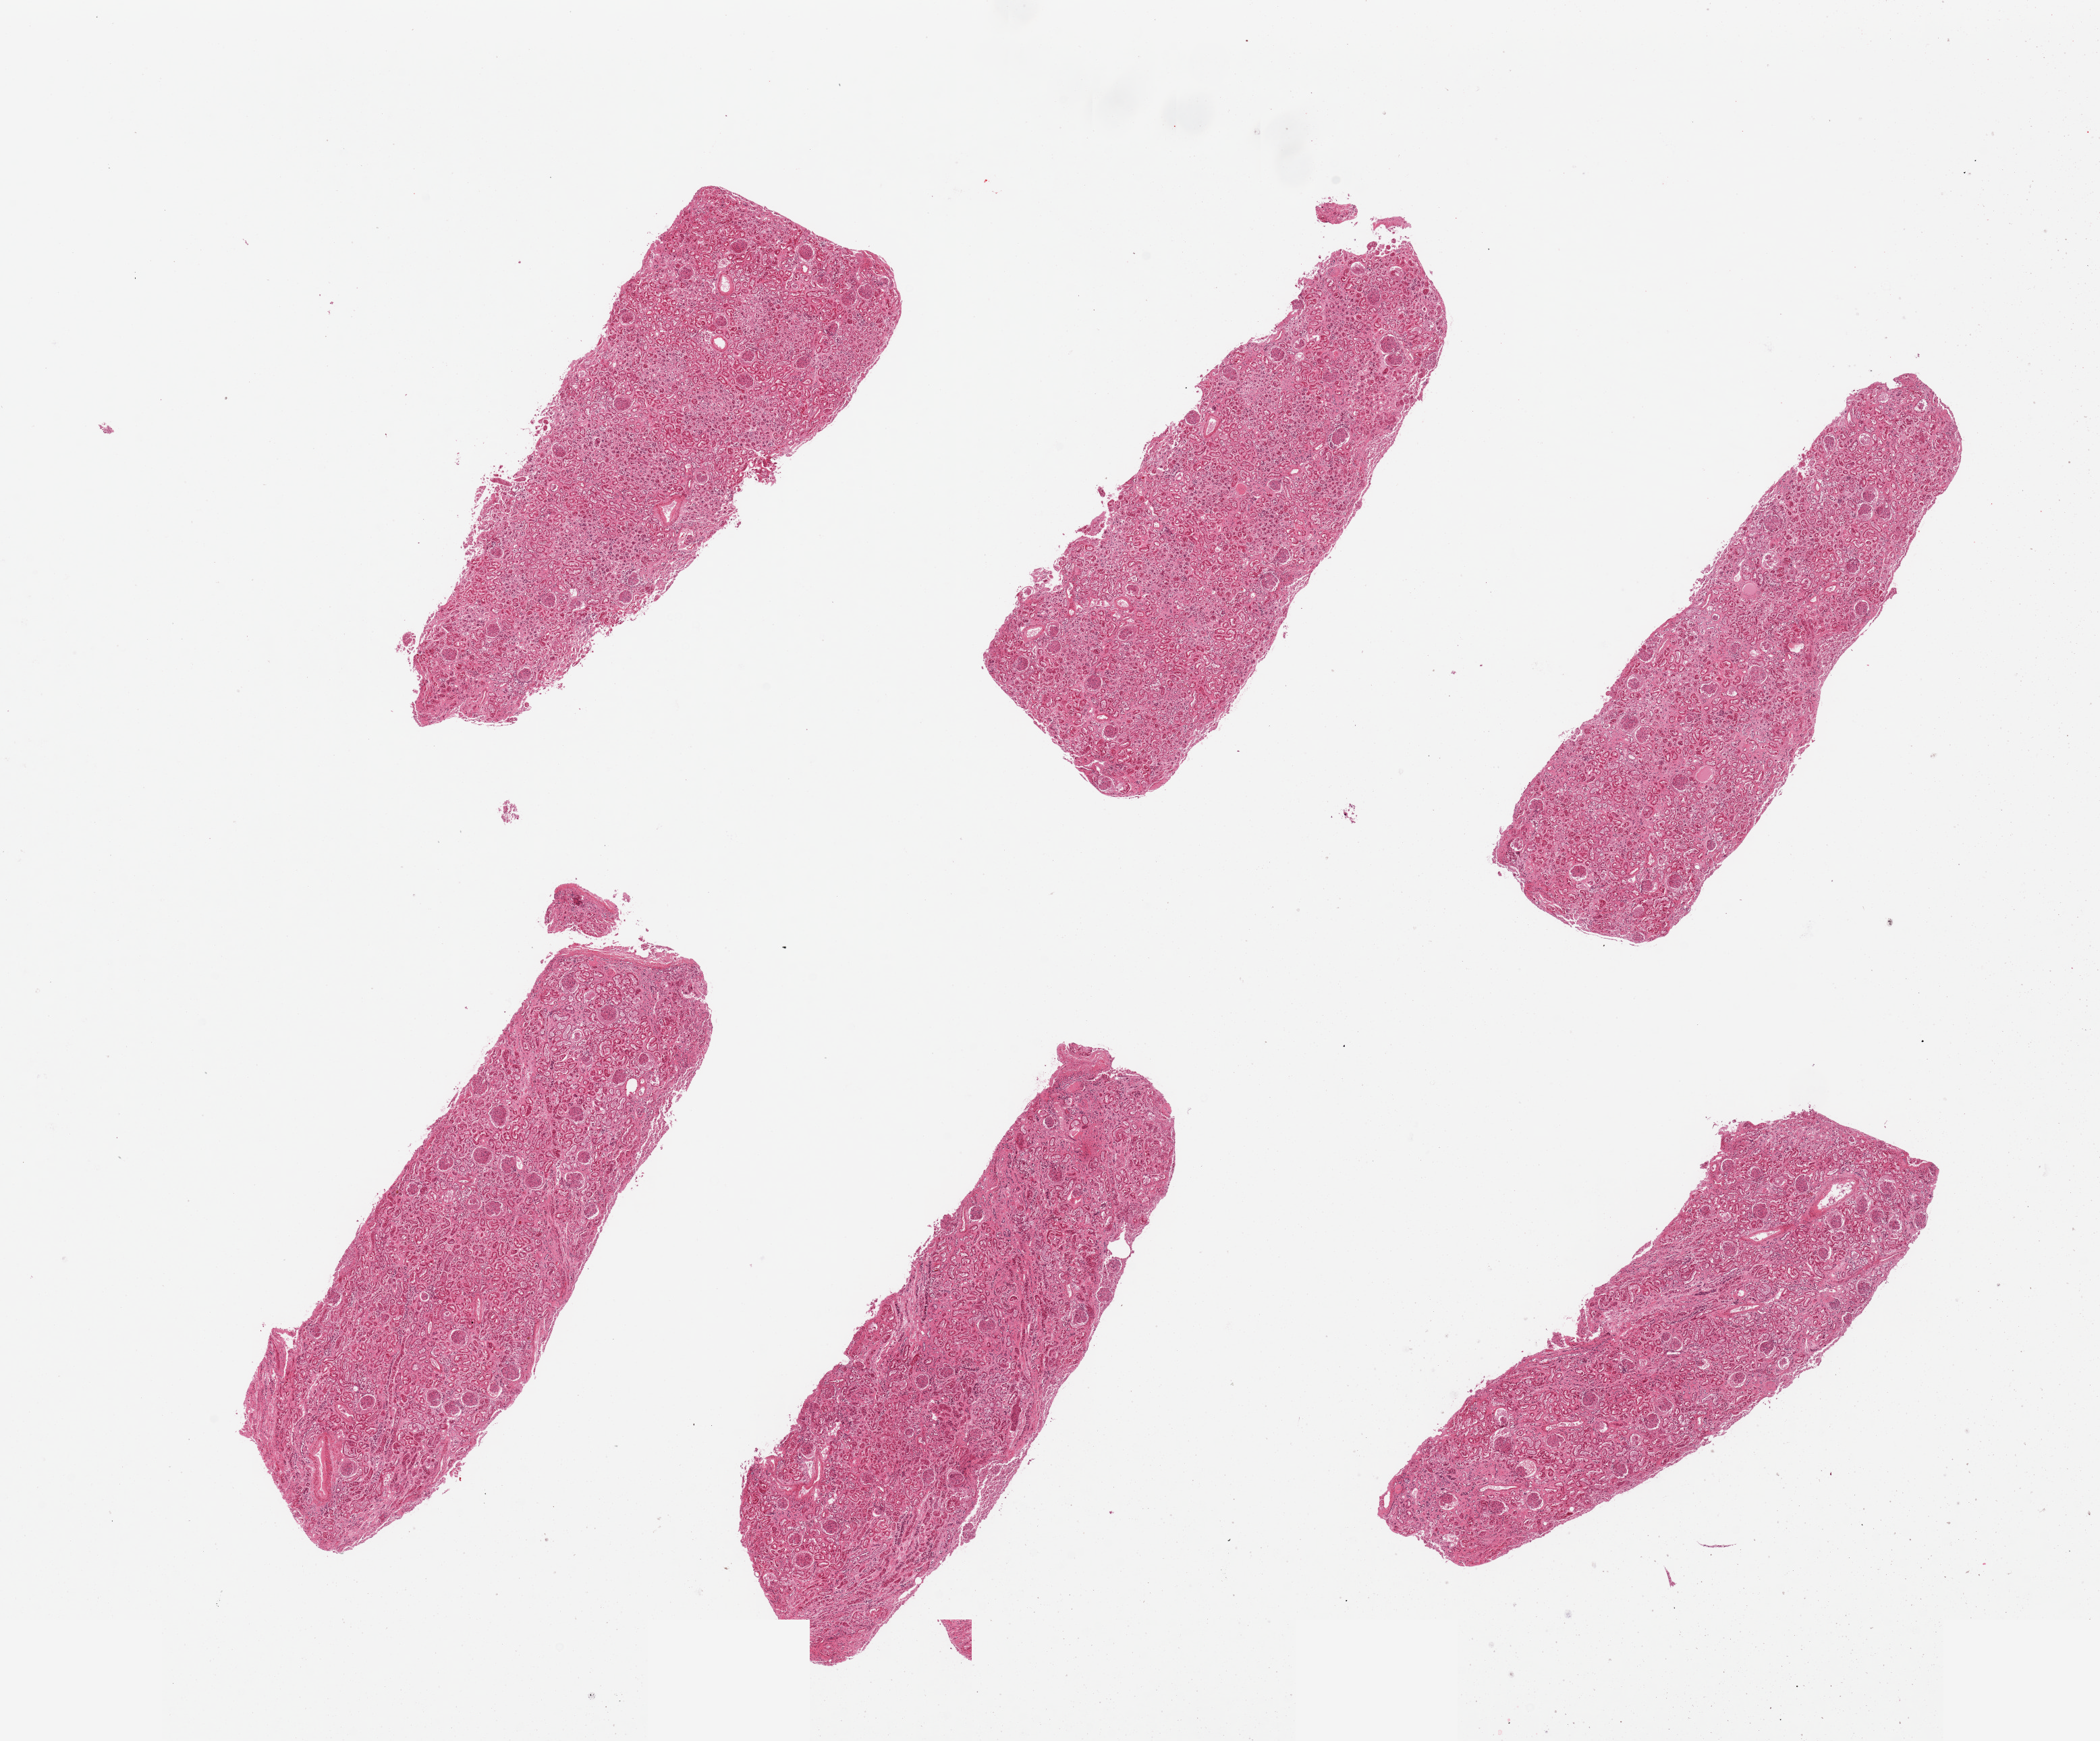
H&E whole-slide image, low-resolution overview of the scanned area, about 24.6 x 20.4 mm (slide scanned at 20x). PAXgene-fixed, paraffin-embedded tissue. Target tissue: renal cortex. Donor tissue sample. Donor: male.
• pathologist's review note for this sample: 6 pieces; membranoproliferative changes and interstitial fibrosis